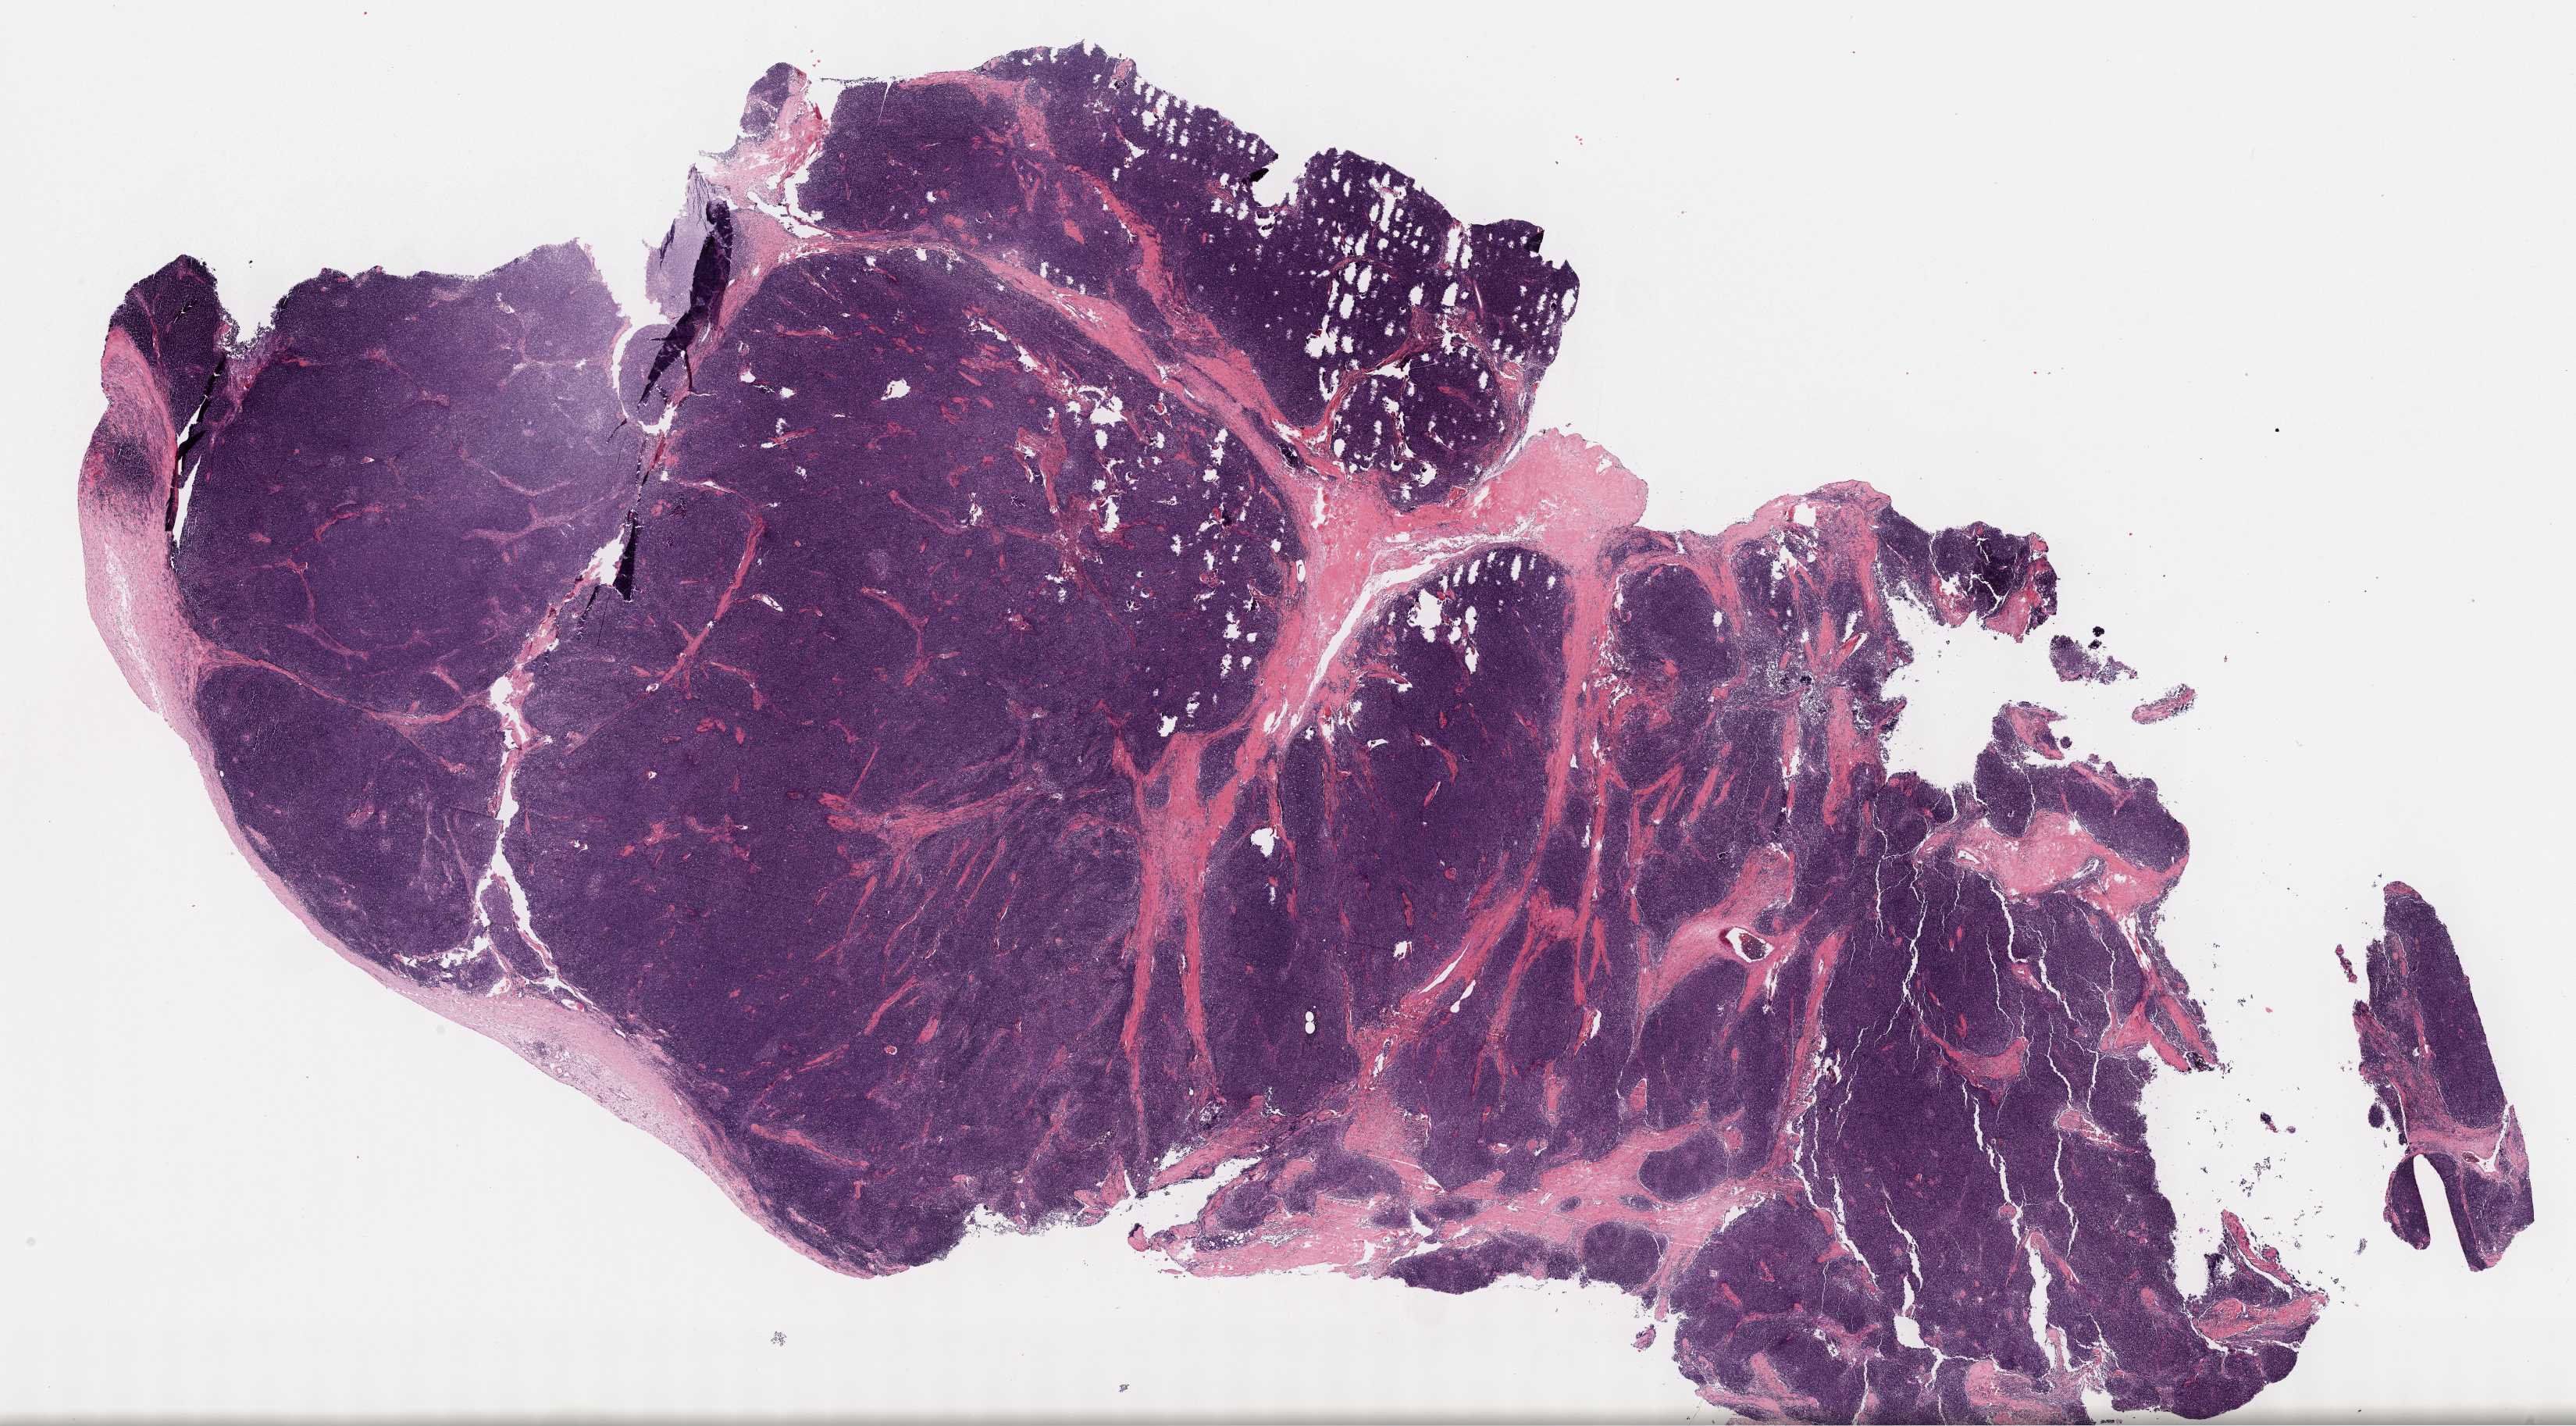
Whole-slide histology image, H&E-stained — a low-resolution overview of the entire scanned area, about 26.7 x 14.8 mm (acquisition: 40x scan), FFPE section, sample: primary tumour, thymus. Female, age 48 years at initial diagnosis.
Pathologic diagnosis: Thymoma, type B2, malignant.